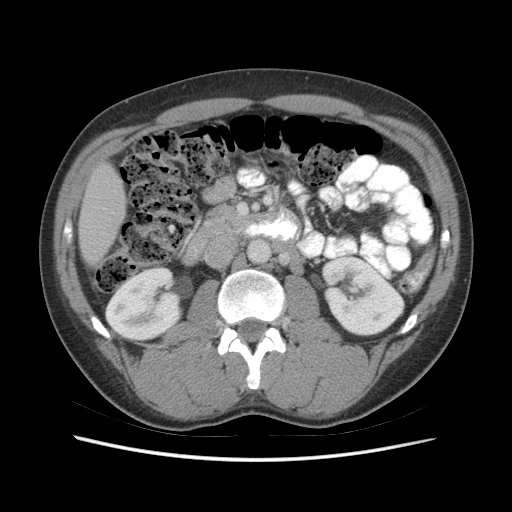
Contrast-enhanced abdominal CT (liver protocol), one axial slice; slice 14 of 73 in the series (ordered by position); 140 kVp; soft-tissue window (W 400 / L 40 HU); 2.5 mm slice thickness; 512 × 512 image matrix, field of view 360 × 360 mm. From the clinical record (not read from this slice): diagnosis: hepatocellular carcinoma (patient treated with transarterial chemoembolisation; whether this scan precedes or follows treatment is not stated here); TNM stage (as recorded): Stage-IIIA; Child-Pugh class: A; tumour nodularity: multinodular; tumour size: 6.6 cm.
Outlined on this slice (semi-automatic segmentation, software-assisted and operator-edited):
- liver parenchyma outside the tumour (the mass and vessels are separate outlines, so this box may not span the whole liver): bounding box (x1, y1, x2, y2) in pixels: (78, 162, 124, 264)